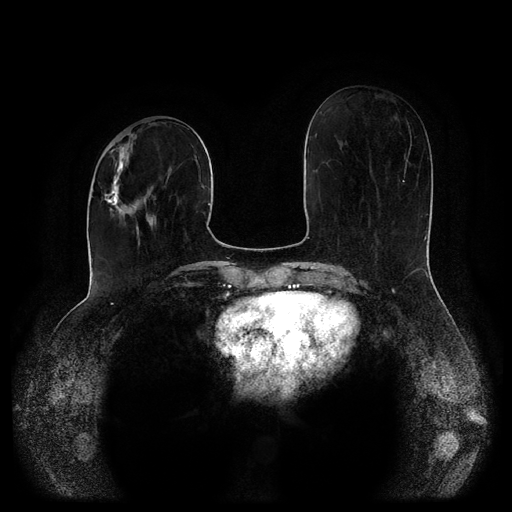
Breast MRI (dynamic contrast-enhanced, multi-phase), one axial slice. Slice 38 of 116 in the series (ordered by position). Dynamic contrast-enhanced series, time point 2 of 5 at this slice position (early post-contrast). 1.5 T. TE 2.6 ms, TR 5.2 ms. 2 mm slice thickness. 512 × 512 image matrix. Patient: female, 52 years.
Annotated regions visible in this slice (semi-automatically segmented with operator editing):
- breast lesion (labelled 'tumour' in the annotation; benign lesions carry a separate 'benign' label): bounding box [x1, y1, x2, y2] px = [100, 144, 133, 224]